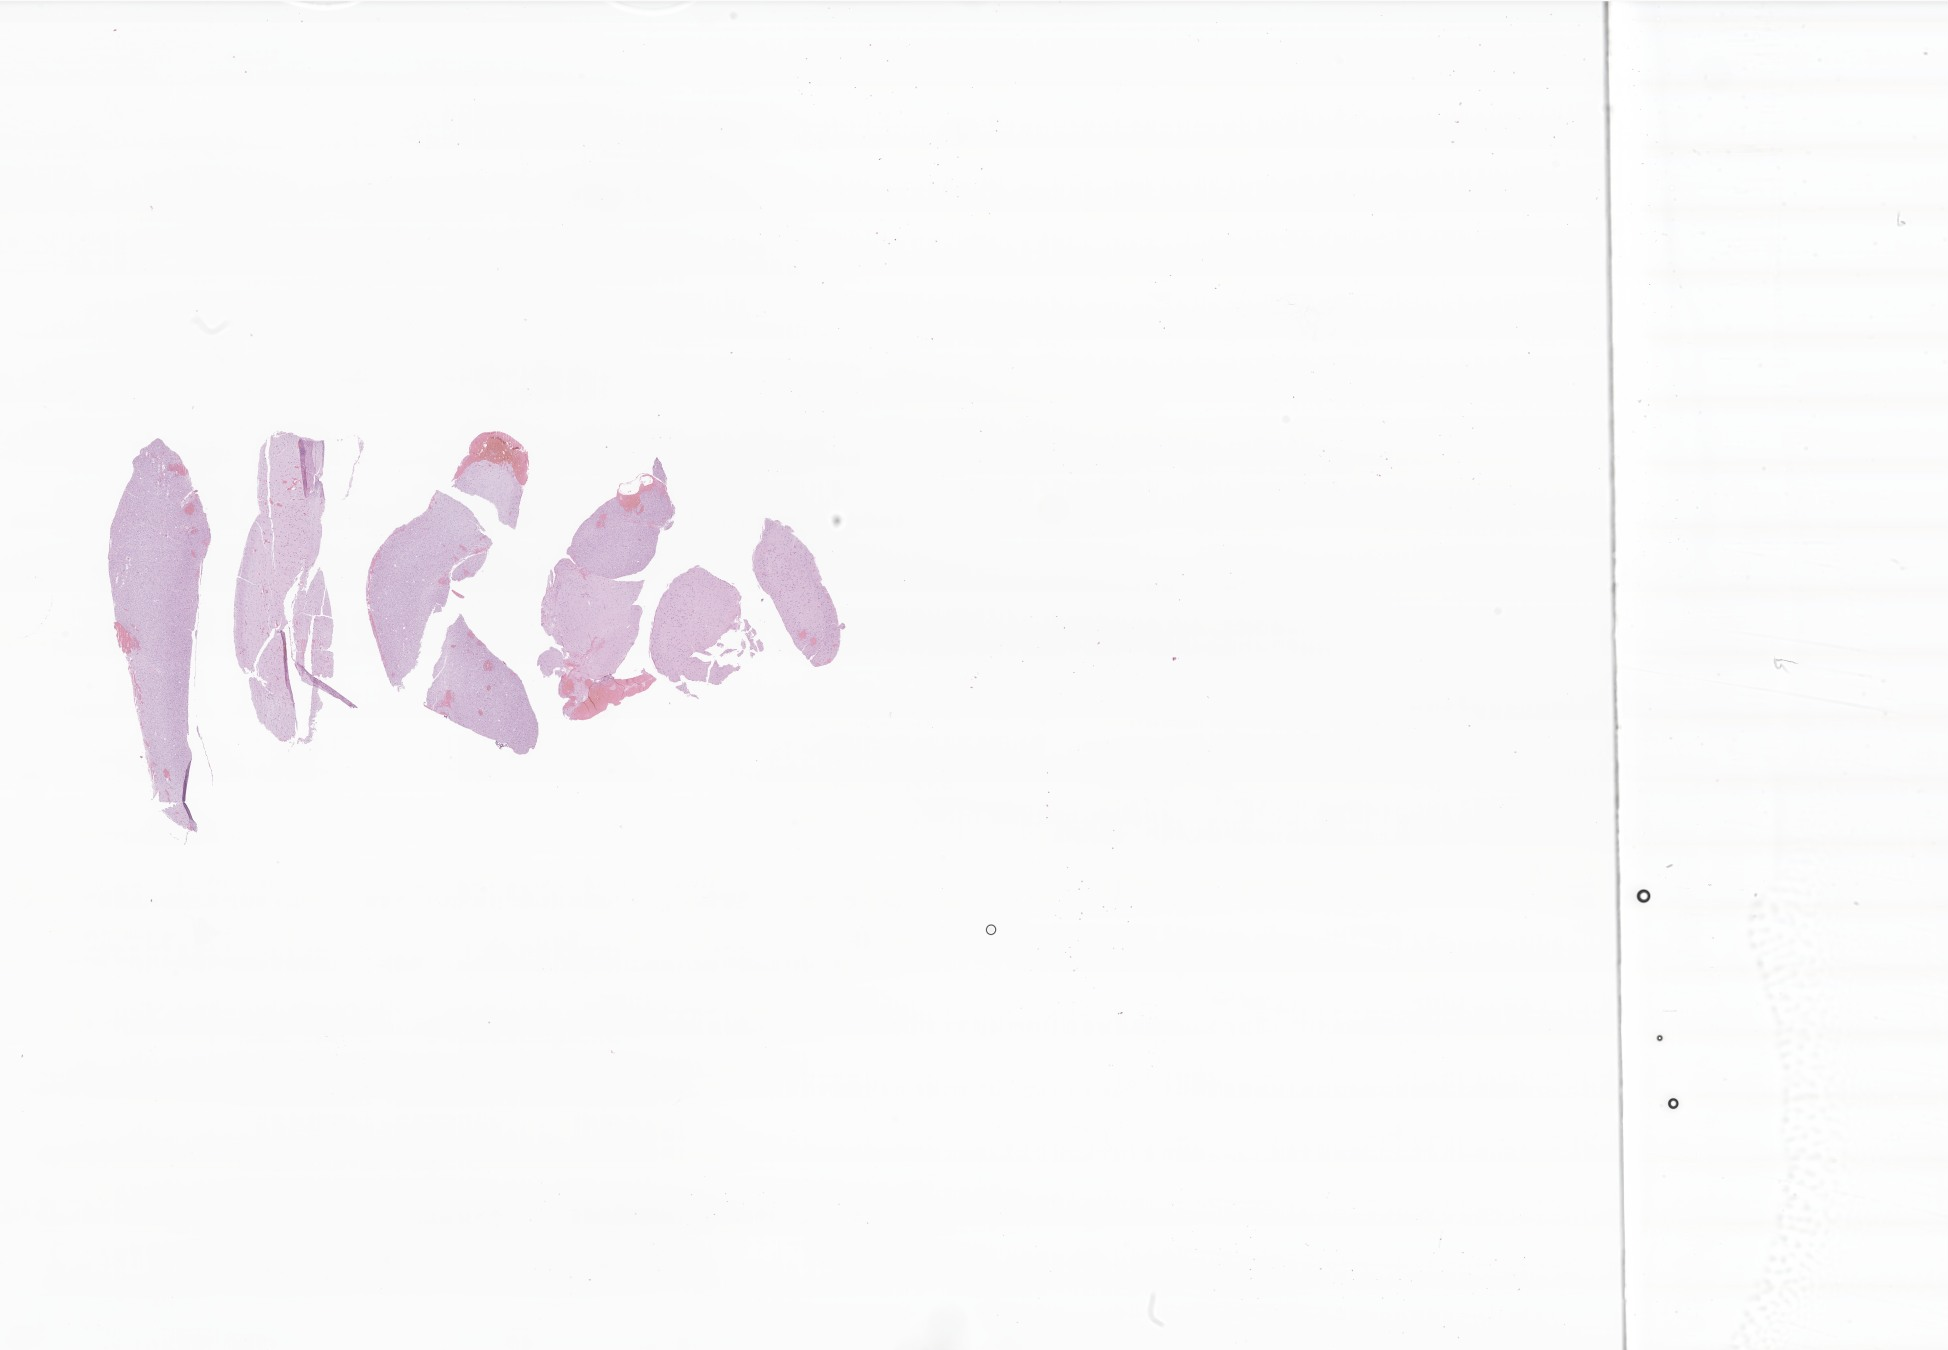
Digitized haematoxylin and eosin-stained section of tumor tissue from the brain, low-resolution overview of the scanned area, about 32.9 x 22.8 mm; FFPE section. Patient: female, age 175 months (14 years 7 months).
Recorded diagnosis: Neoplasm, uncertain whether benign or malignant.